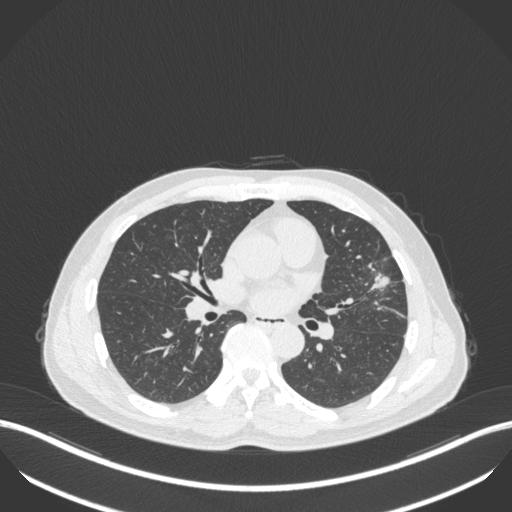
Chest CT, one axial slice. Position 205 of 418 along the scan axis. Reconstruction kernel B31f. 120 kVp. Lung window (W 1500 / L -600 HU). 1 mm slice thickness. 512 × 512 image matrix, field of view 400 × 400 mm. Patient: male, 55 years. Case-level facts recorded for this patient, not image findings: clinical TNM (as recorded): T1c N0 M0; histopathological grade: G2-3.
Outlined on this slice (bounding box drawn by a radiologist):
- lung tumour (recorded histology: adenocarcinoma): bounding box [x1, y1, x2, y2] px = [368, 268, 391, 291]